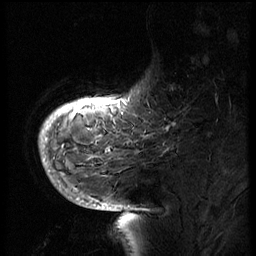
Breast MRI (dynamic contrast-enhanced), one sagittal slice. Slice 12 of 66 in the series (ordered by position). 3 images stored at this slice position (order not interpretable as contrast timing). 1.5 T. TE 4.2 ms, TR 8.9 ms. 2.5 mm slice thickness. 256 × 256 image matrix, field of view 200 × 200 mm. Patient: female, 56 years. Case-level facts recorded for this patient, not image findings: setting: breast cancer imaged before/during neoadjuvant chemotherapy.
Outlined on this slice (semi-automatically segmented with operator editing):
- analysis volume of interest (the breast-tissue region the enhancement analysis was run in; not a lesion): bounding box <129,62,194,127> (left, top, right, bottom; pixels)
- tumour enhancement mask (voxels above the 140 % enhancement threshold inside the analysis volume of interest): <129,101,177,126>